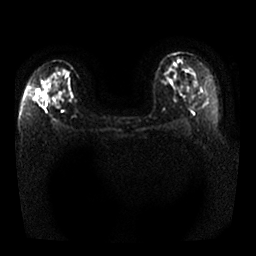
Breast MRI, one axial slice. Position 14 of 25 along the scan axis. Diffusion-weighted series; image 2 of 4 stored at this slice position (different b-values; order by instance number). 1.5 T. 4 mm slice thickness. 256 × 256 image matrix, field of view 340 × 340 mm. Female patient.
Structures marked on this image (manually delineated by an expert):
- tumour on diffusion-weighted imaging: bounding box [x1, y1, x2, y2] px = [37, 85, 53, 102]